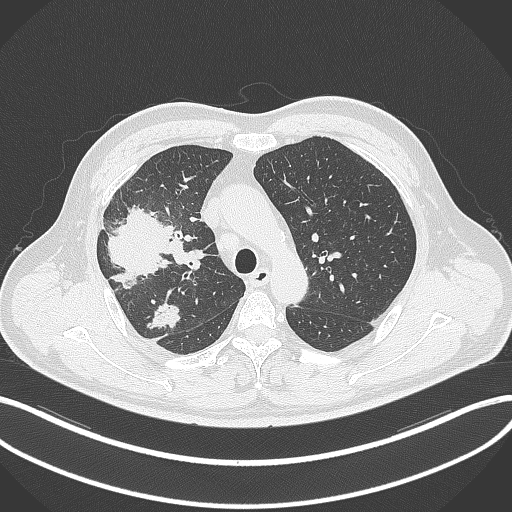
Chest CT, one axial slice. Position 238 of 348 along the scan axis. Reconstruction kernel B70f. 120 kVp. Lung window (W 1500 / L -600 HU). 1 mm slice thickness. 512 × 512 image matrix, field of view 400 × 400 mm. Male patient, age 55 years. From the clinical record (not read from this slice): clinical TNM (as recorded): T3 N2 M1.
Structures marked on this image (rectangle marked by the reading radiologist):
- lung tumour (recorded histology: adenocarcinoma): bounding box (x1, y1, x2, y2) in pixels: (103, 201, 173, 292)